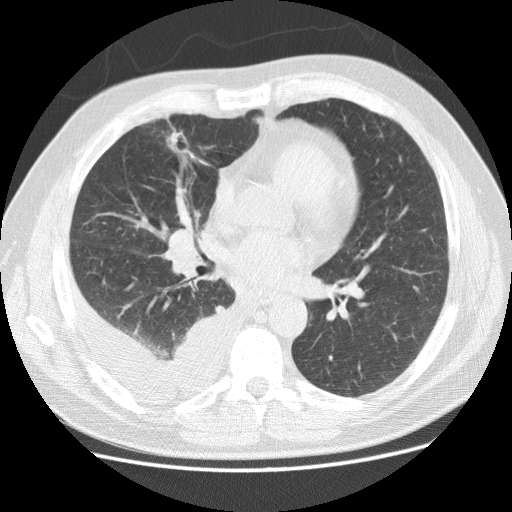
Low-dose screening chest CT, one axial slice; slice 62 of 142 in the series (ordered by position); reconstruction kernel STANDARD; lung window (W 1500 / L -600 HU); 2.5 mm slice thickness; 512 × 512 image matrix, field of view 380 × 380 mm.
Annotated regions visible in this slice (outlined manually by an expert reader):
- lesion 1 (tumor, middle lobe of right lung): bounding box <167,130,191,158> (left, top, right, bottom; pixels)